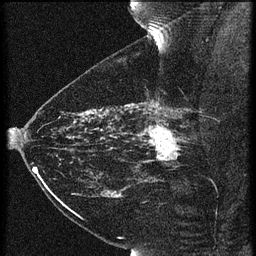
Breast MRI (dynamic contrast-enhanced), one sagittal slice; position 44 of 60 along the scan axis; 3 images stored at this slice position (order not interpretable as contrast timing); 1.5 T; TE 4.2 ms, TR 21.3 ms; 1.5 mm slice thickness; 256 × 256 image matrix. Patient: female, 43 years. Case-level facts recorded for this patient, not image findings: setting: breast cancer imaged before/during neoadjuvant chemotherapy; receptor status: HER2-positive.
Annotated regions visible in this slice (semi-automatic segmentation, software-assisted and operator-edited):
- analysis volume of interest (the breast-tissue region the enhancement analysis was run in; not a lesion): bounding box <119,114,189,173> (left, top, right, bottom; pixels)
- tumour enhancement mask (voxels above the 90 % enhancement threshold inside the analysis volume of interest): <138,114,180,163>